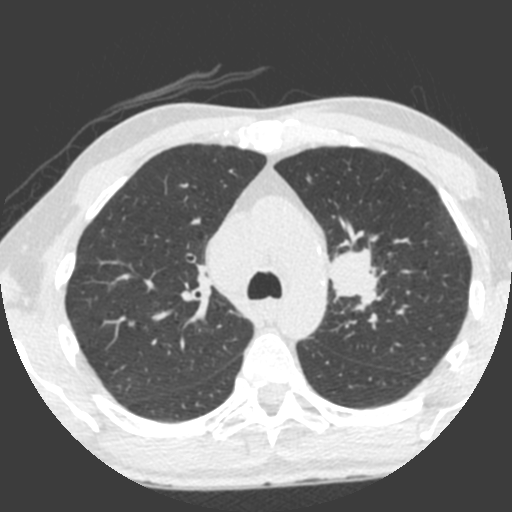
Low-dose screening chest CT, axial slice, third annual screen, lung window (W 1500 / L -600 HU), 2 mm slice thickness, standard (soft-tissue) reconstruction kernel (B), slice 152 of 212 in the series, 512 × 512 image matrix, field of view 315 × 315 mm. Male participant, aged 55 years at enrolment. Current smoker at enrolment.
Expert-annotated lung lesion, bounding box (x1, y1, x2, y2) in pixels: (308, 232, 389, 322). The exam's reader record, not a measurement of the box and not confirmed to be the same lesion: non-calcified nodule or mass ≥4 mm, left upper lobe, 49 × 29 mm, spiculated (stellate) margins, soft tissue attenuation, pre-existing on the prior screen: yes; interval growth: yes. Official screen result: positive, other. Lung cancer was diagnosed 0 days after this screen: small cell carcinoma, NOS, left upper lobe, undifferentiated (G4), stage IV (AJCC 6th edition), 60 mm at pathology.